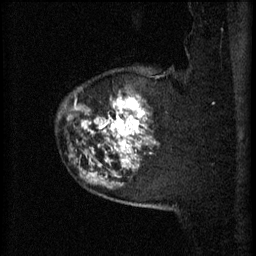
Breast MRI (dynamic contrast-enhanced), one sagittal slice. Slice 52 of 60 in the series (ordered by position). 3 images stored at this slice position (order not interpretable as contrast timing). 1.5 T. TE 4.2 ms, TR 11 ms. 256 × 256 image matrix, field of view 180 × 180 mm. Female patient, age 52 years.
Annotated regions visible in this slice (semi-automatic segmentation, software-assisted and operator-edited):
- analysis volume of interest (the breast-tissue region the enhancement analysis was run in; not a lesion): bounding box (x1, y1, x2, y2) in pixels: (81, 70, 163, 157)
- tumour enhancement mask (voxels above the 70 % enhancement threshold inside the analysis volume of interest): (83, 96, 156, 157)